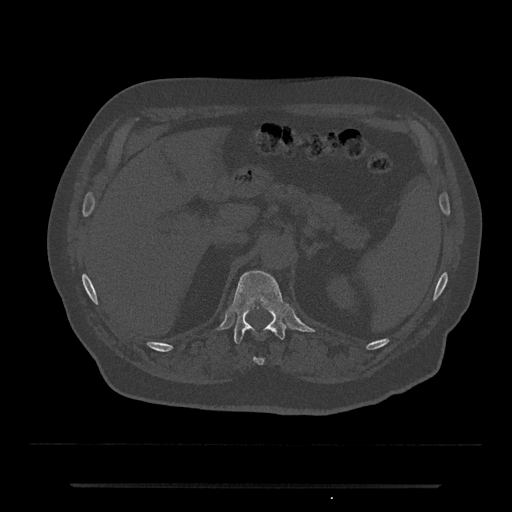
CT including the spine, one axial slice; slice 603 of 797 in the series (ordered by position); bone window (W 1800 / L 400 HU); 0.5 mm slice thickness; 512 × 512 image matrix. Male patient, age 80 years. From the clinical record (not read from this slice): primary cancer: prostate.
Outlined on this slice (semi-automatically segmented with operator editing):
- T11 vertebra: bounding box [x1, y1, x2, y2] px = [253, 357, 264, 365]
- T12 vertebra: [230, 270, 289, 344]